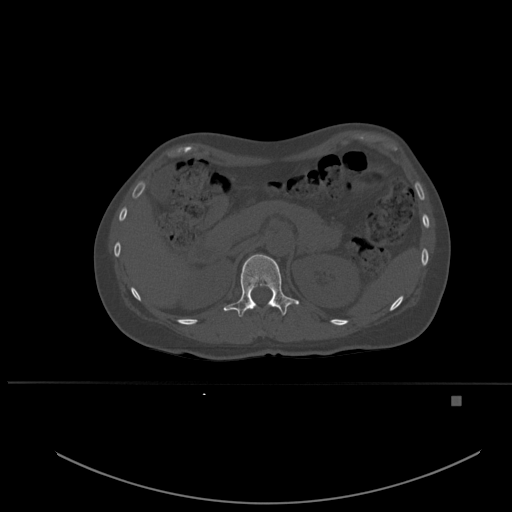
CT including the spine, one axial slice; slice 256 of 651 in the series (ordered by position); bone window (W 1800 / L 400 HU); 512 × 512 image matrix. Female patient, age 49 years. From the clinical record (not read from this slice): primary cancer: breast; vertebrae with lytic lesions (as recorded): L3, T12, L4.
Structures marked on this image (semi-automatically segmented with operator editing):
- T12 vertebra: bounding box [x1, y1, x2, y2] px = [223, 254, 299, 317]